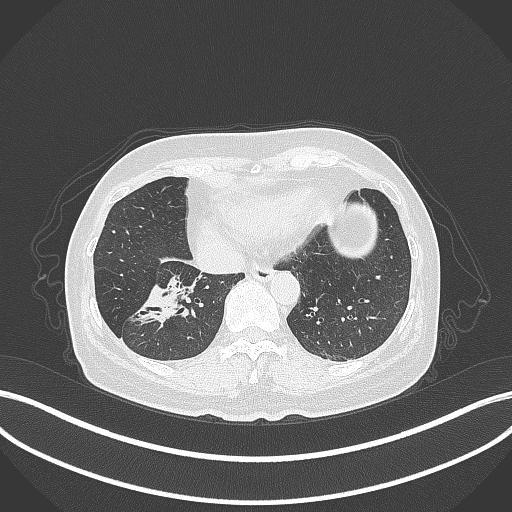
Chest CT, one axial slice; position 113 of 429 along the scan axis; 120 kVp; lung window (W 1500 / L -600 HU); 512 × 512 image matrix, field of view 400 × 400 mm. Patient: female, 67 years. From the clinical record (not read from this slice): clinical TNM (as recorded): T1c N1 M0; histopathological grade: G2-3.
Structures marked on this image (rectangle marked by the reading radiologist):
- lung tumour (recorded histology: adenocarcinoma): bounding box <131,278,192,328> (left, top, right, bottom; pixels)